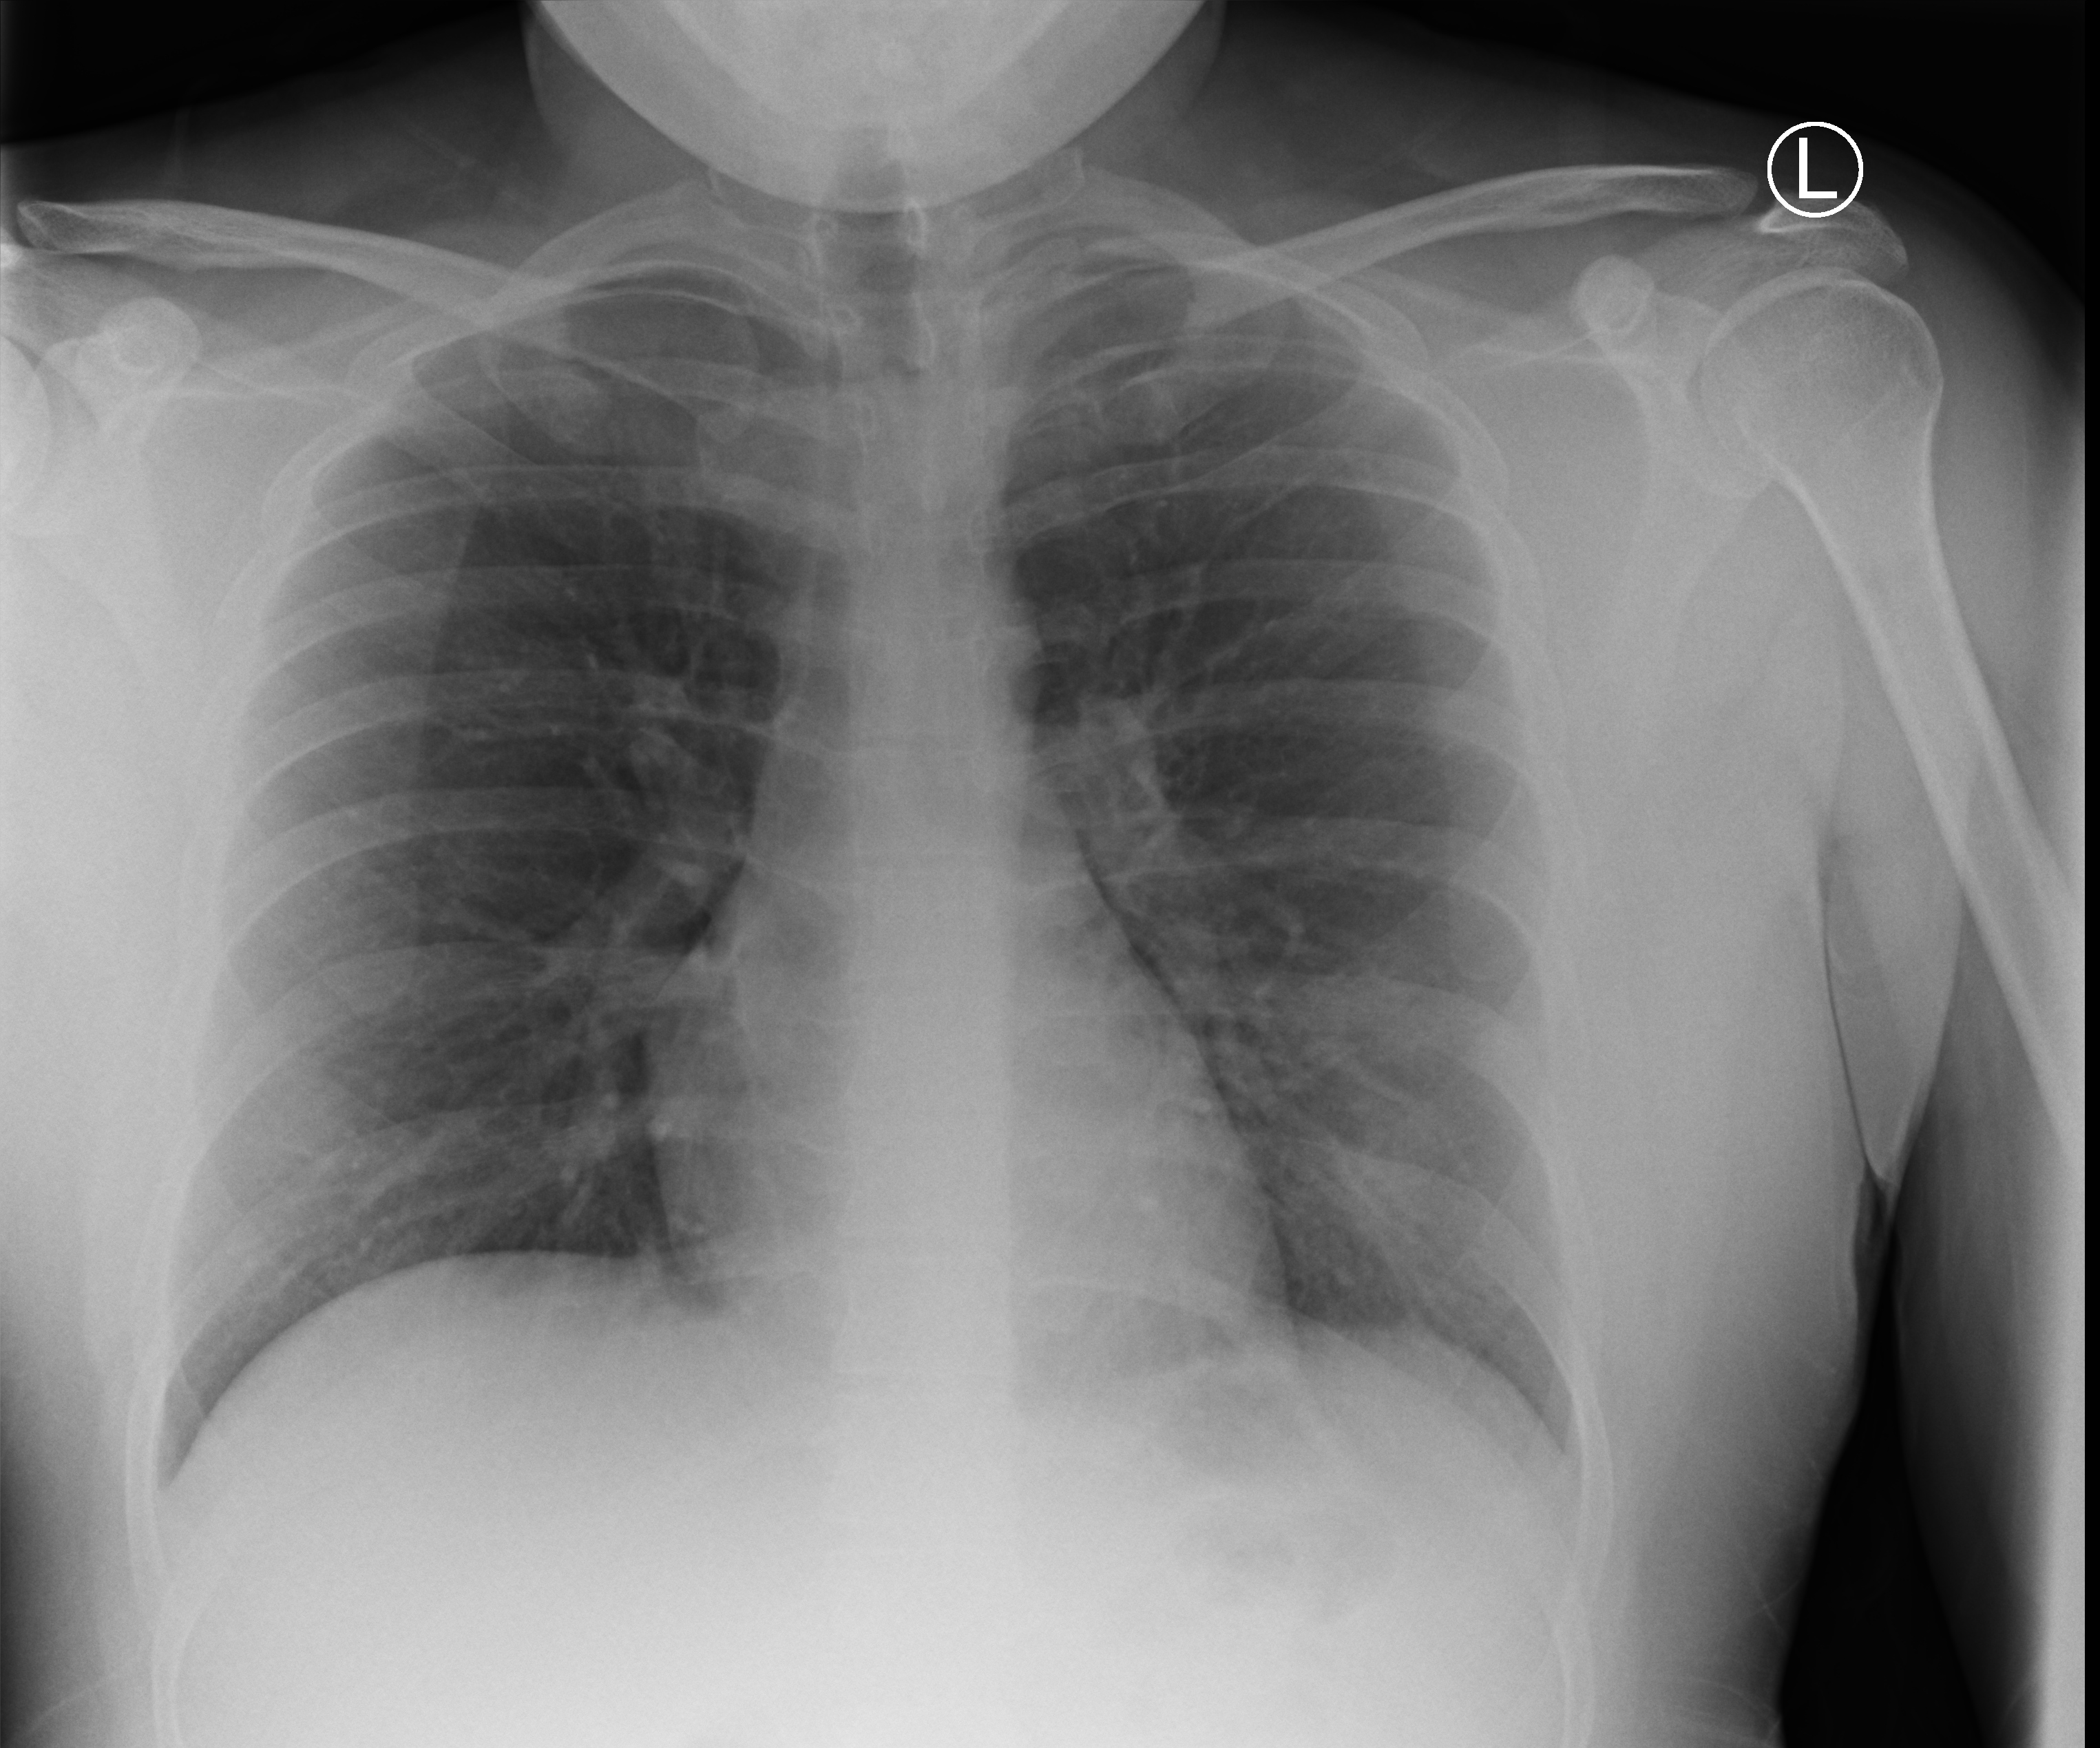
Portable chest radiograph; anteroposterior (AP) projection. Male patient hospitalised with COVID-19, age 18–59 years.
Admission-level facts for this patient (not findings on this image; timing relative to this image not recorded): mechanically ventilated during this hospital stay: no.